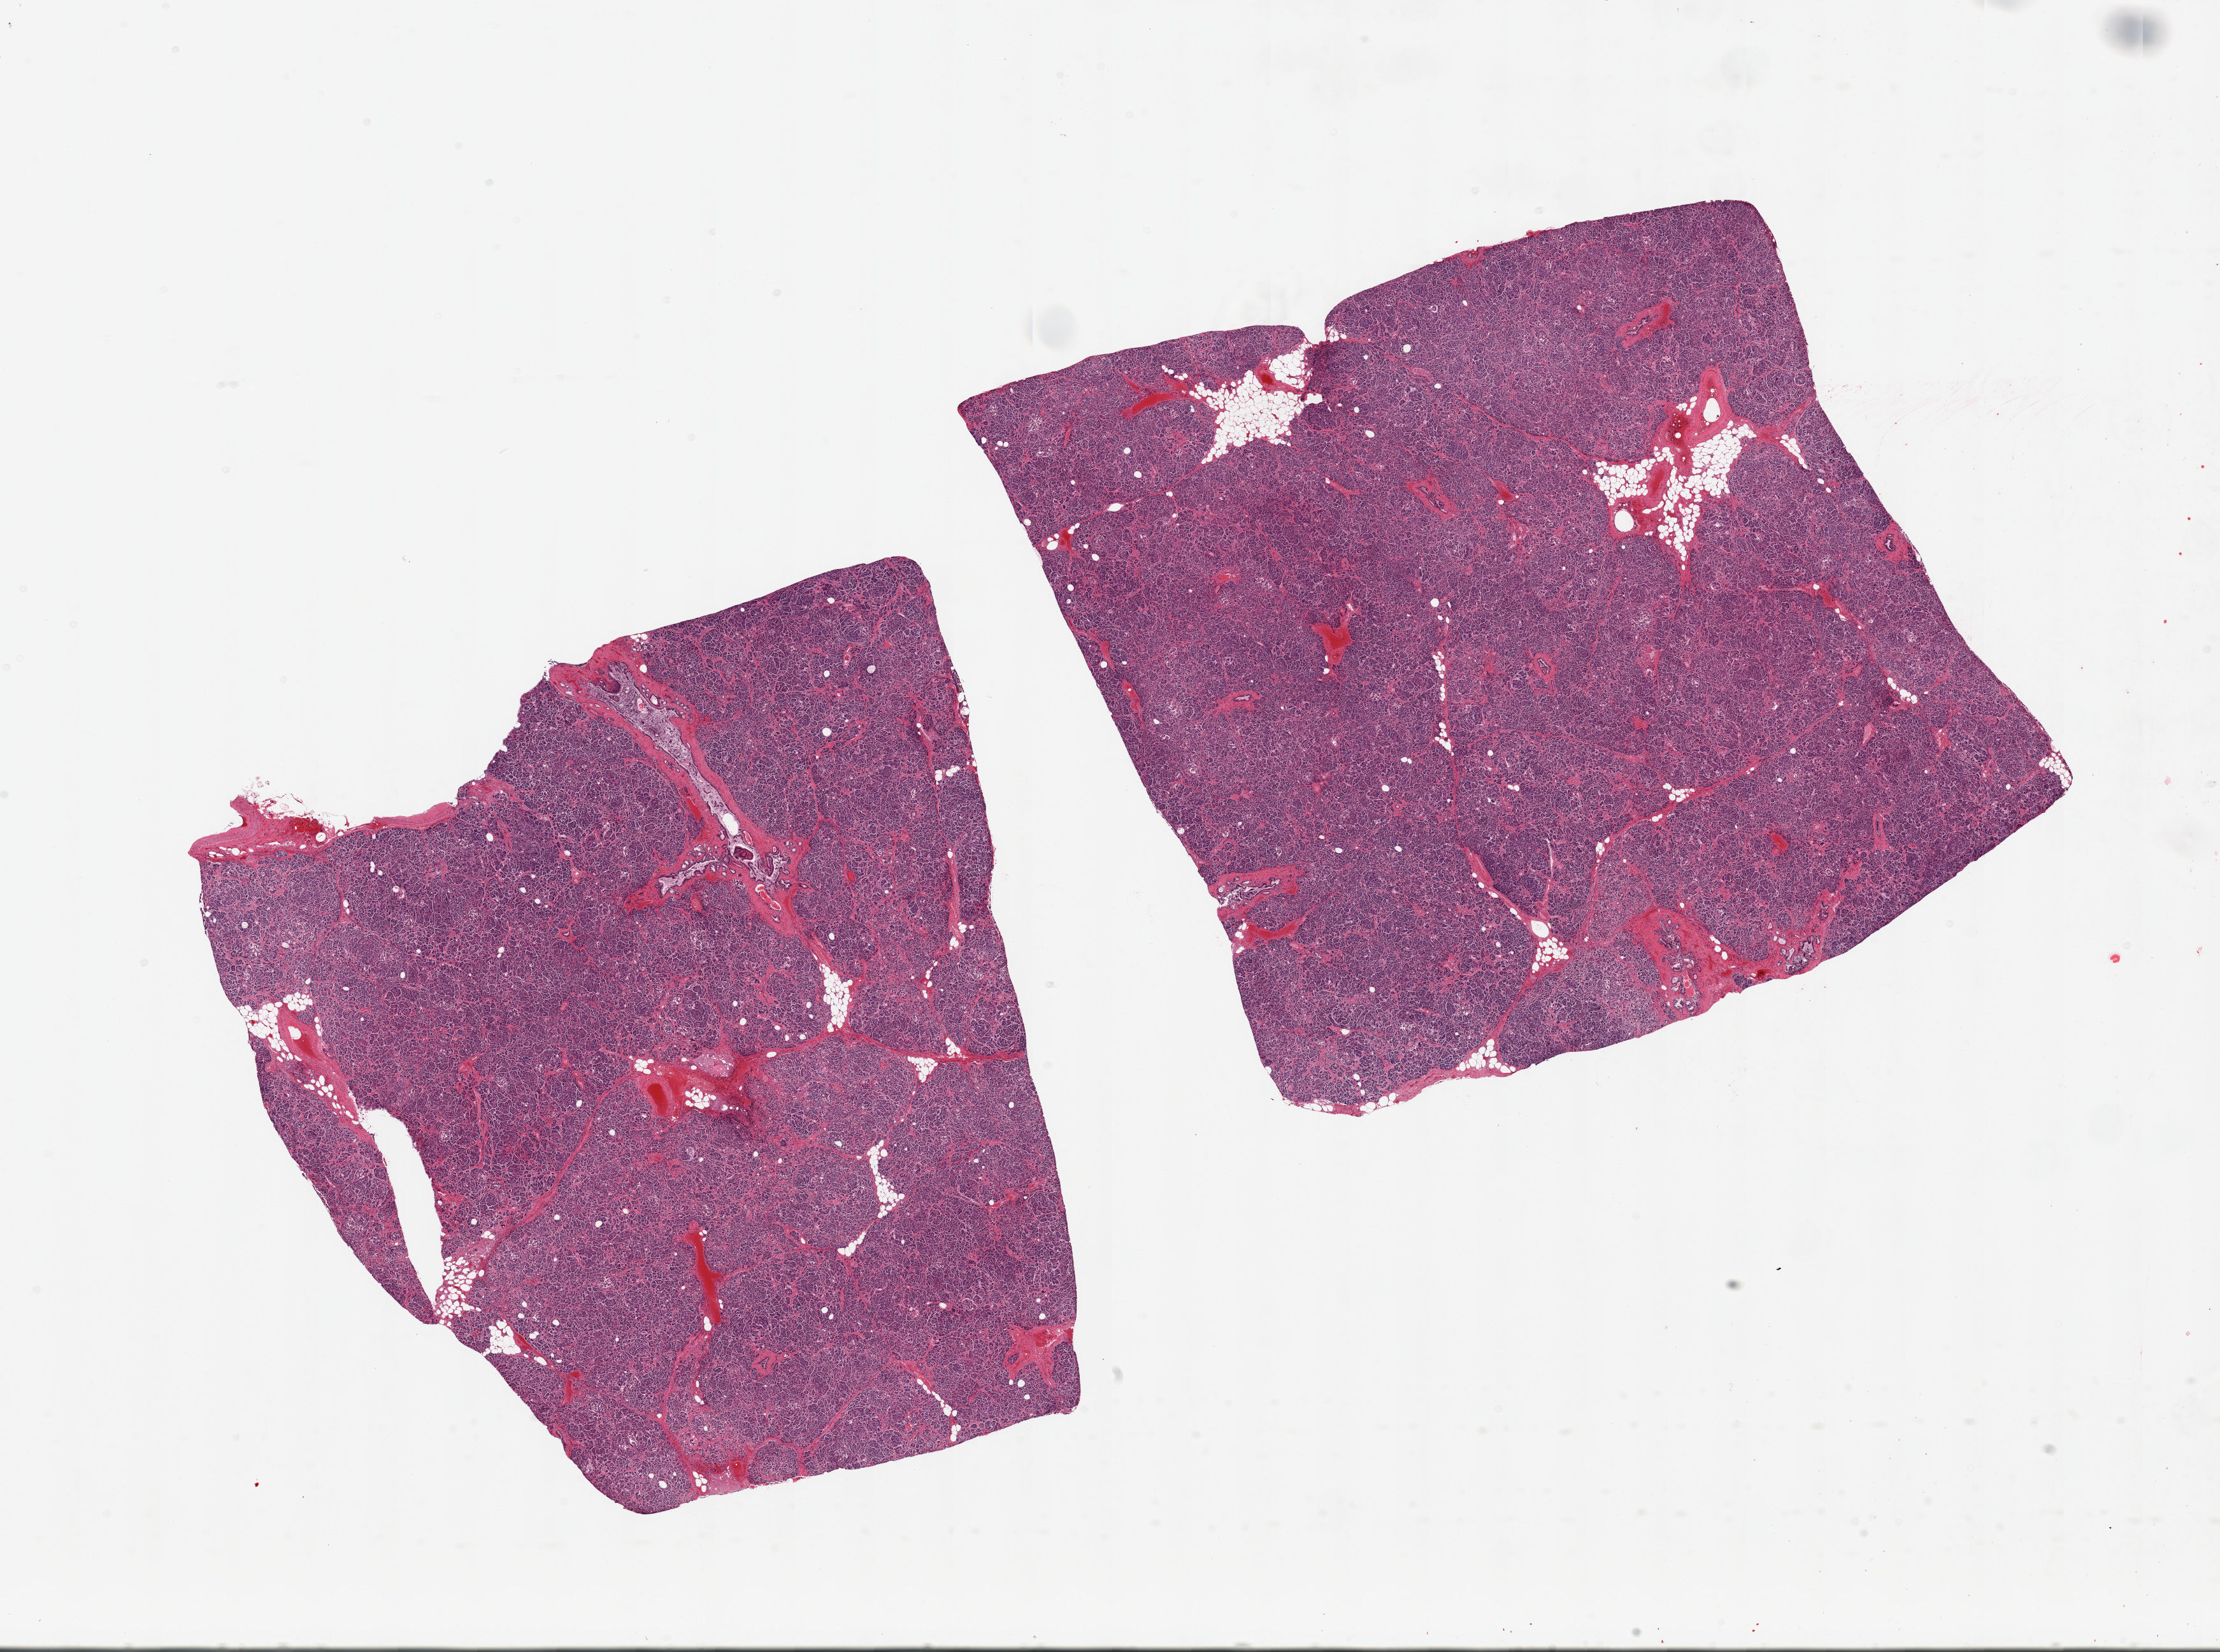
H&E whole-slide image — low-resolution overview of the scanned area, about 27.6 x 20.5 mm; PAXgene-fixed paraffin-embedded (PFPE) section; sampled site (target tissue): pancreas; tissue donor sample. Donor: male.
Reviewer comment on this tissue sample: 2 pieces; 10% internal fat.